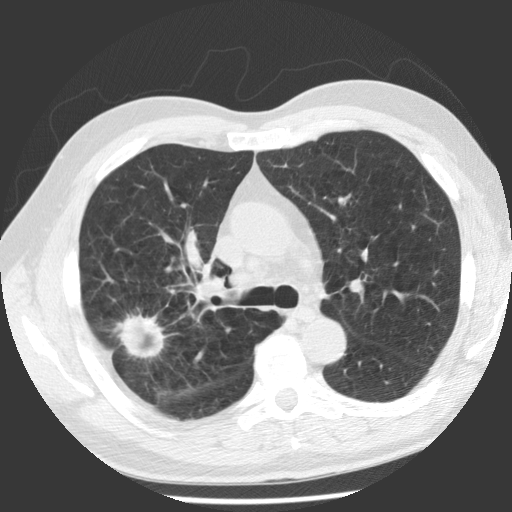
Low-dose screening chest CT, axial slice. Baseline screening round. Lung window (W 1500 / L -600 HU). 2.5 mm slice thickness. Standard (soft-tissue) reconstruction kernel (STANDARD). 512 × 512 image matrix. Male participant, aged 62 years at enrolment.
Expert-annotated lung lesion, box from (x=104, y=299) to (x=177, y=368) px. The screening reader recorded 2 non-calcified nodules or masses ≥4 mm on this exam (right upper lobe, right upper lobe); which of them this box marks is not recorded. Later outcome: lung cancer diagnosed 71 days after this screen — adenocarcinoma, NOS, right upper lobe, poorly differentiated (G3), stage IV (AJCC 6th edition), 30 mm at pathology.